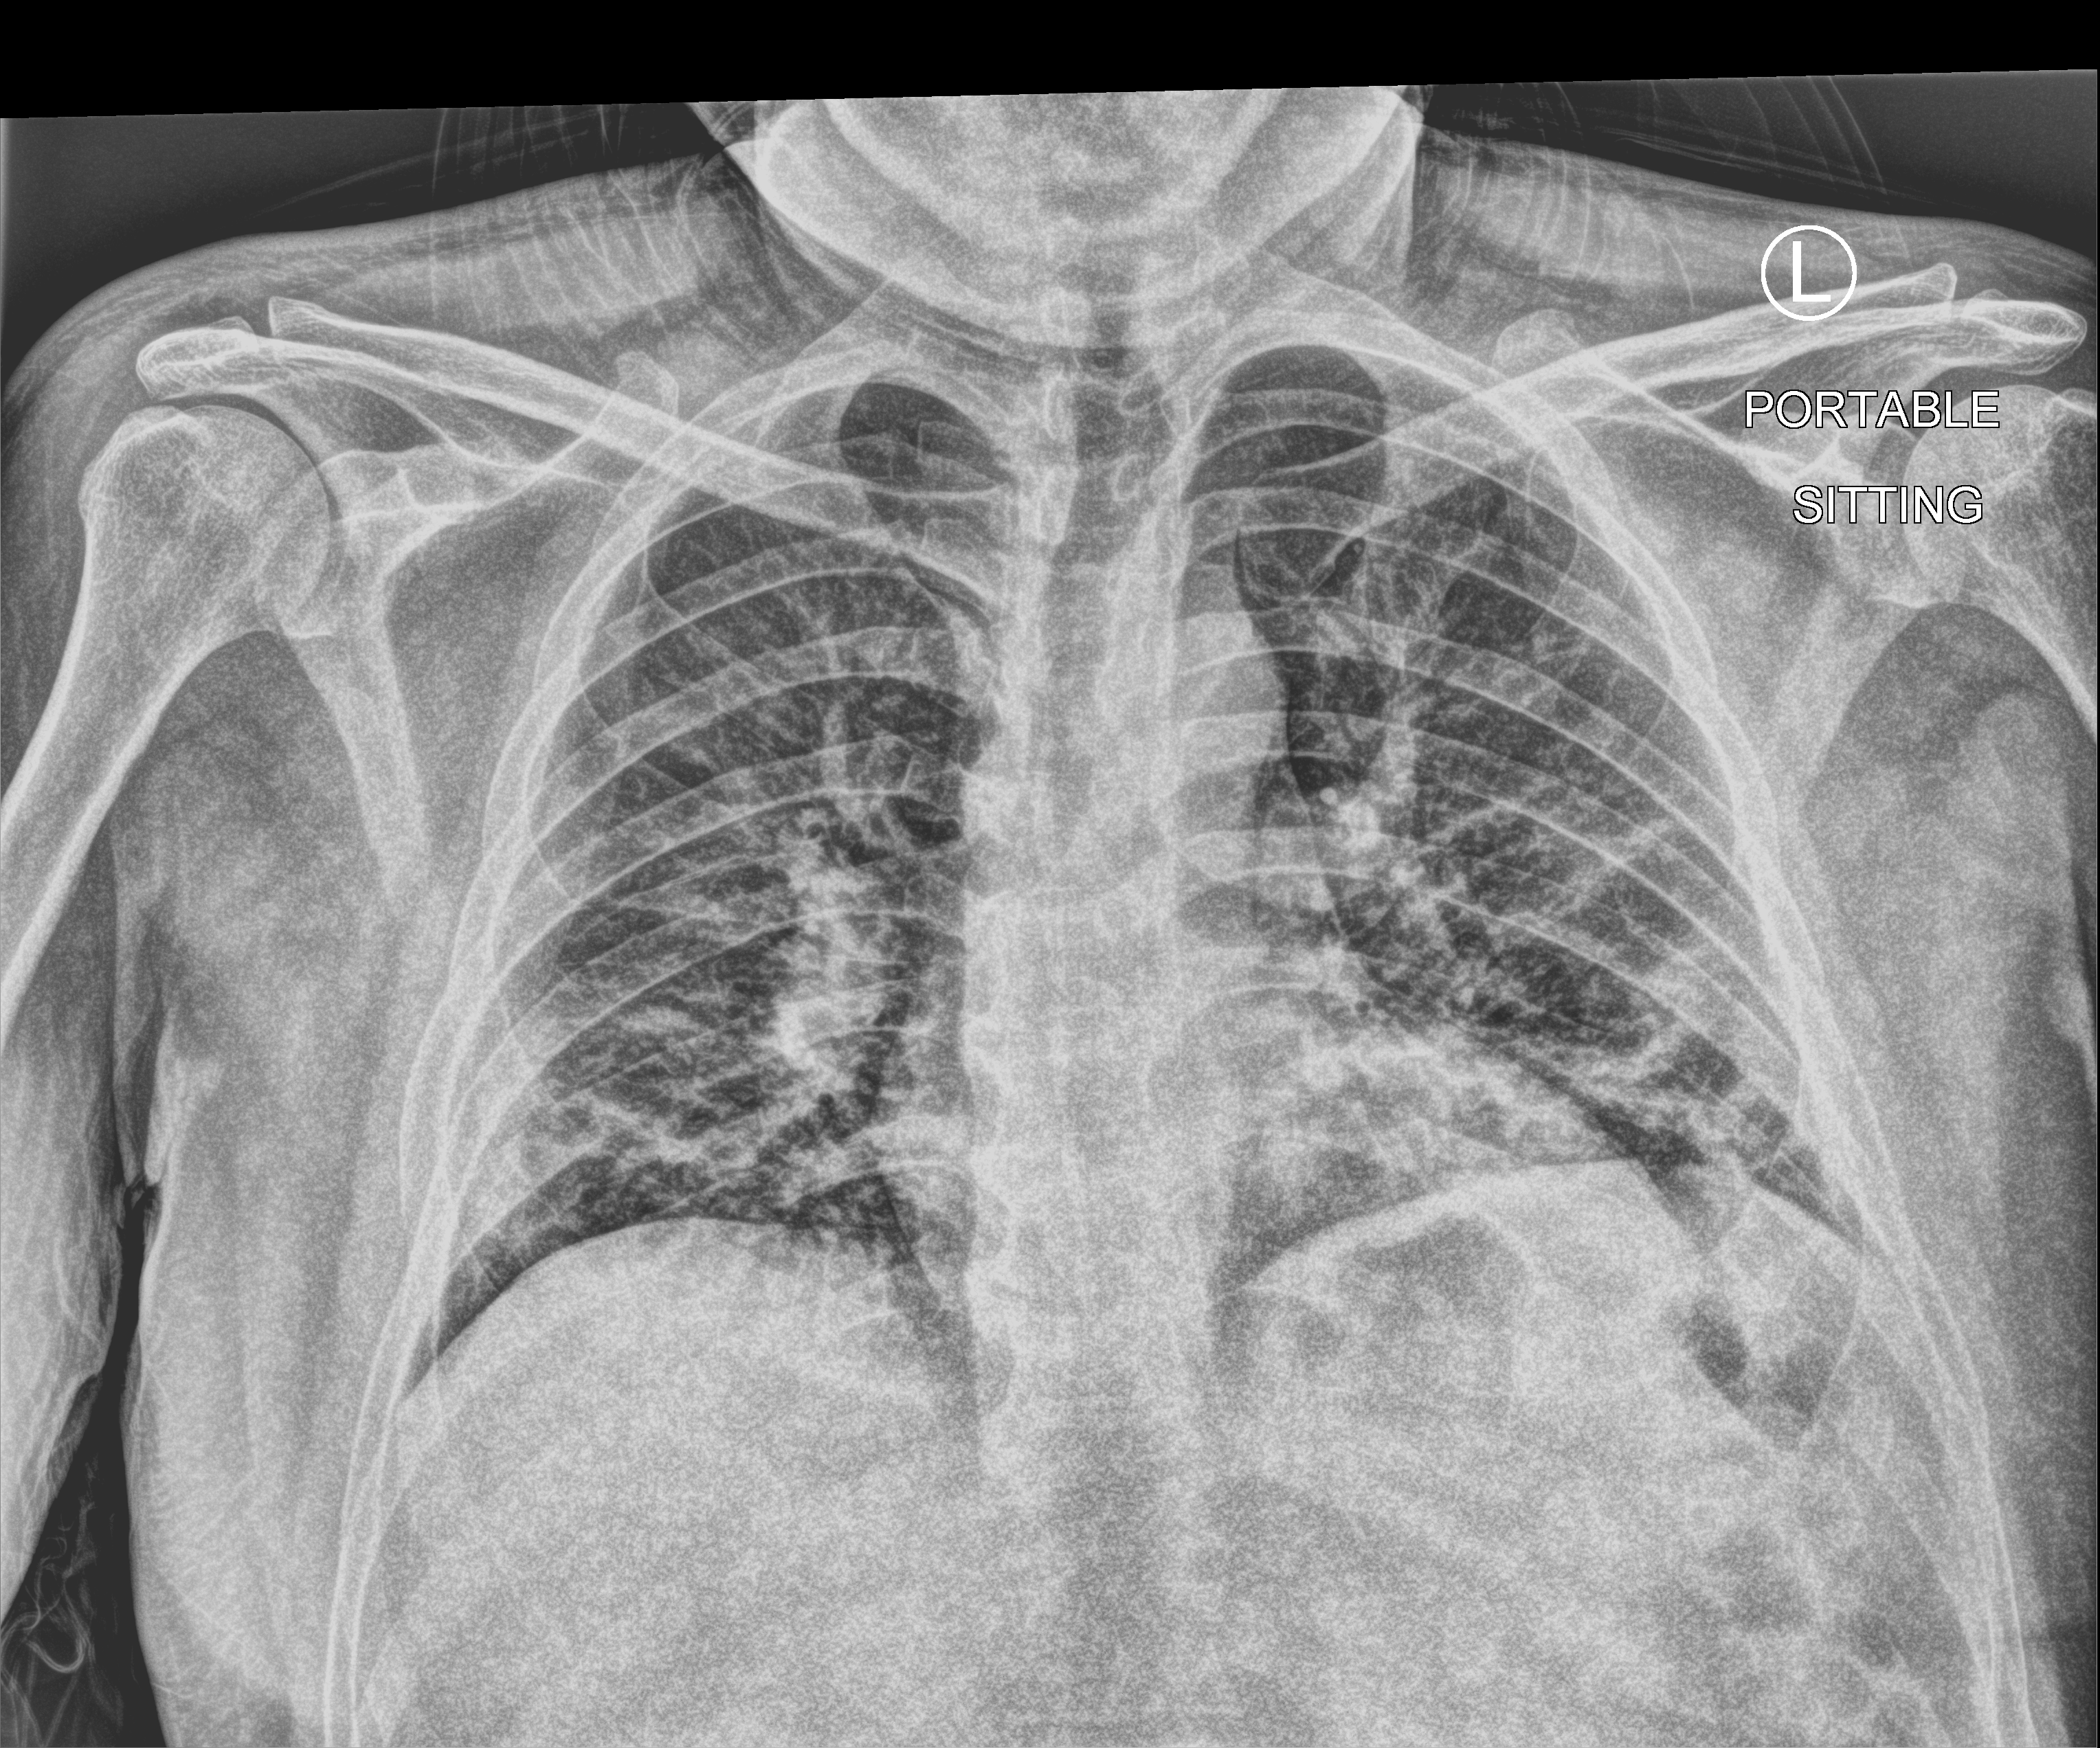
Portable chest radiograph; anteroposterior (AP) projection. Male patient hospitalised with COVID-19, age 18–59 years.
Admission-level facts for this patient (not findings on this image; timing relative to this image not recorded): admitted to intensive care during this hospital stay: no; mechanically ventilated during this hospital stay: no.